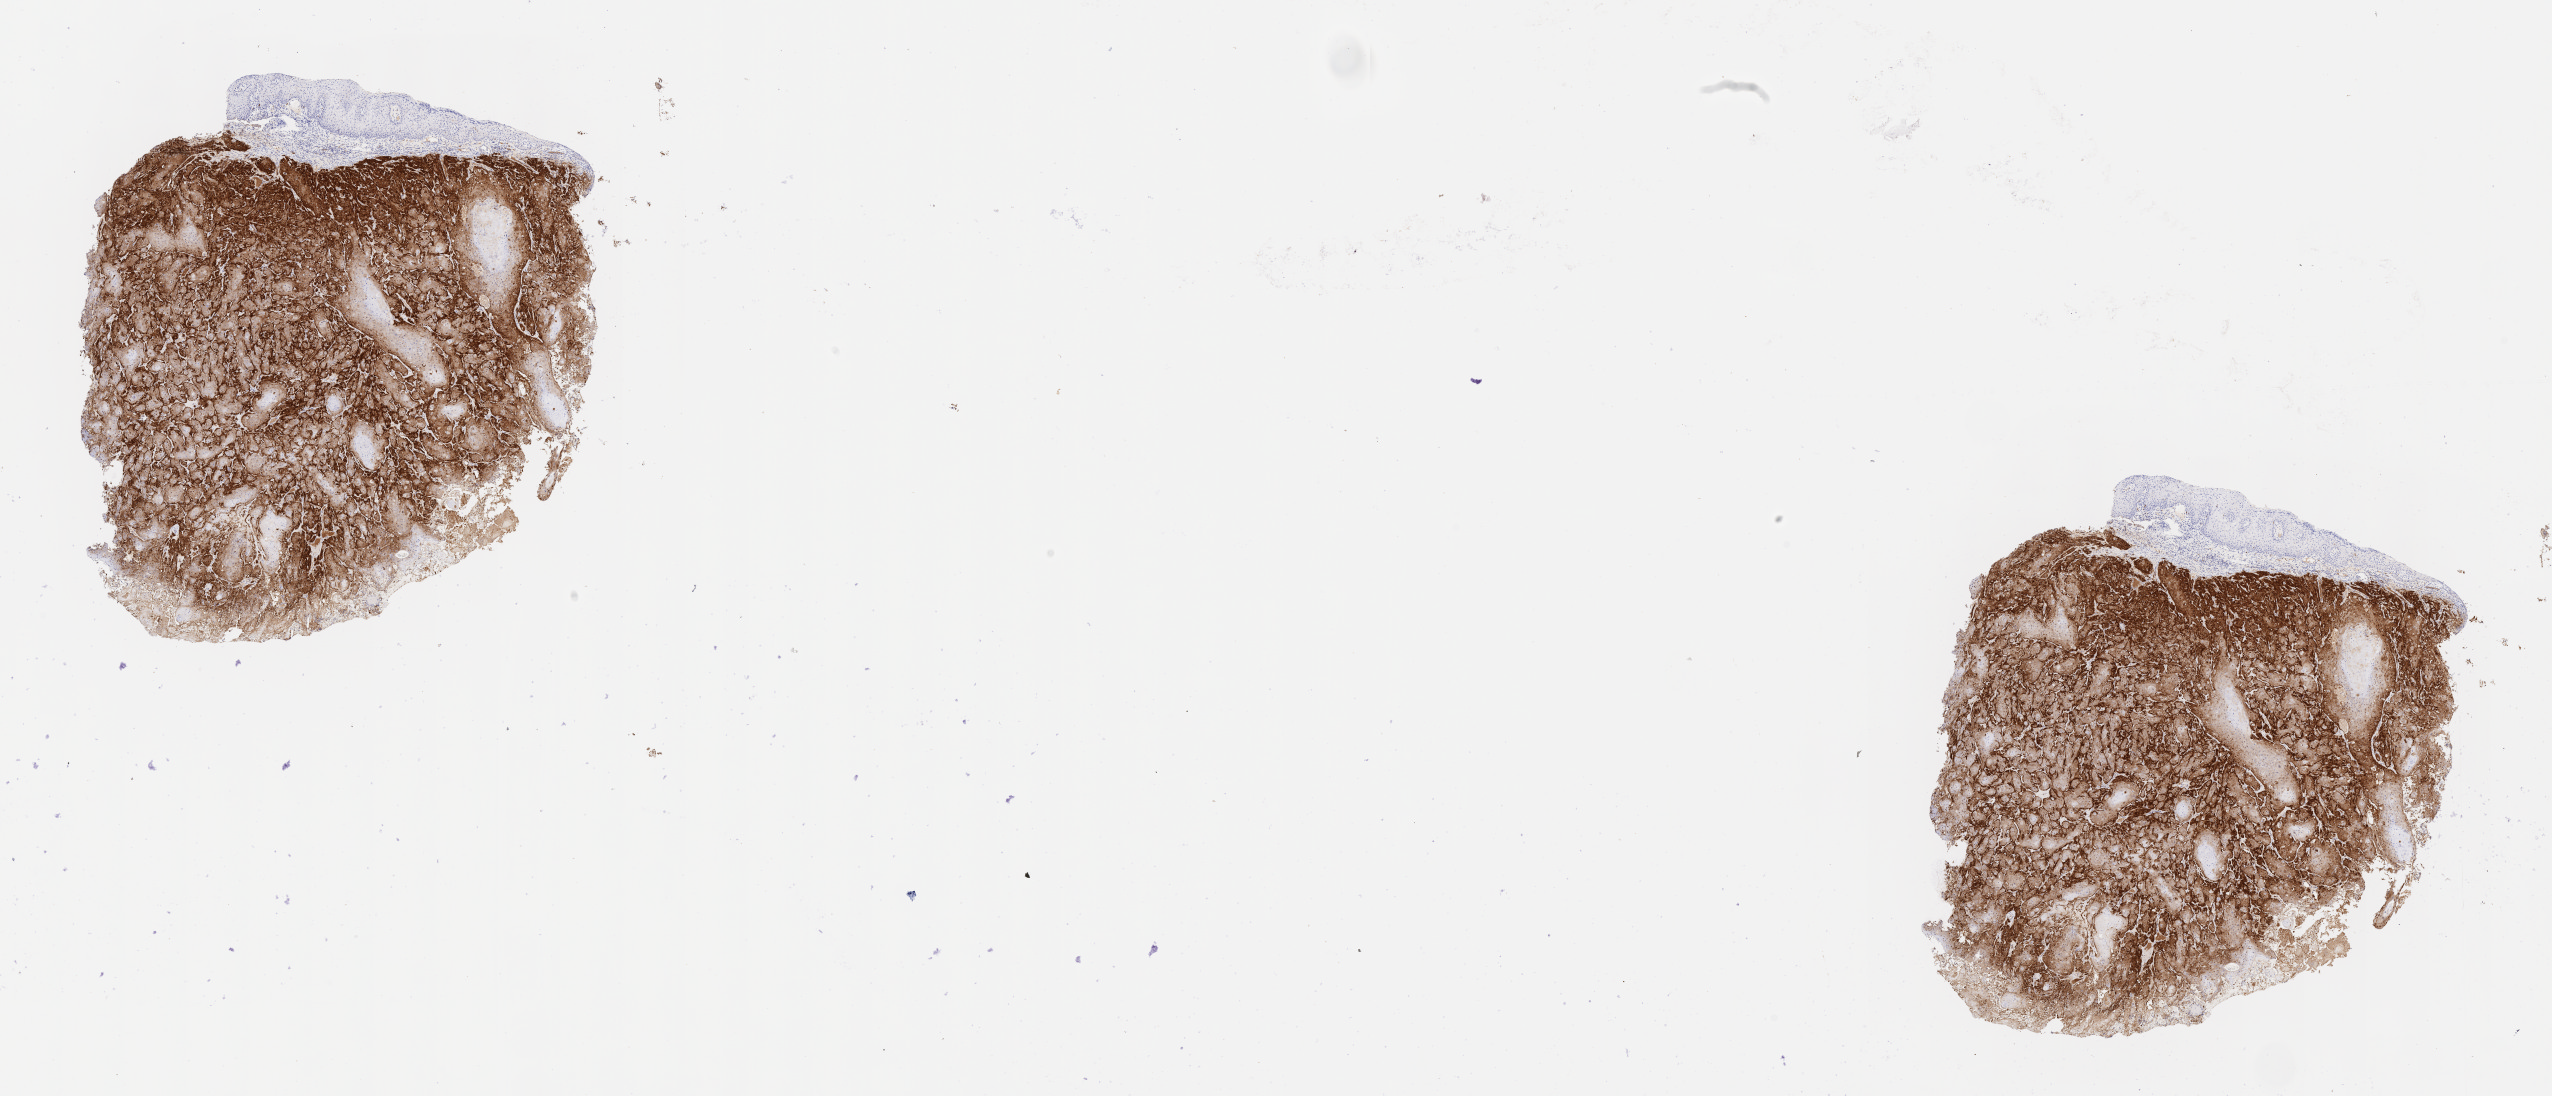
Immunohistochemistry (IHC) whole-slide image stained for p16 (p16INK4a), a low-resolution overview of the entire scanned area, about 20.6 x 8.9 mm, specimen: tumor tissue, site: cervix. Patient: female, aged 43.
Diagnosis: Squamous cell carcinoma, keratinizing, NOS.